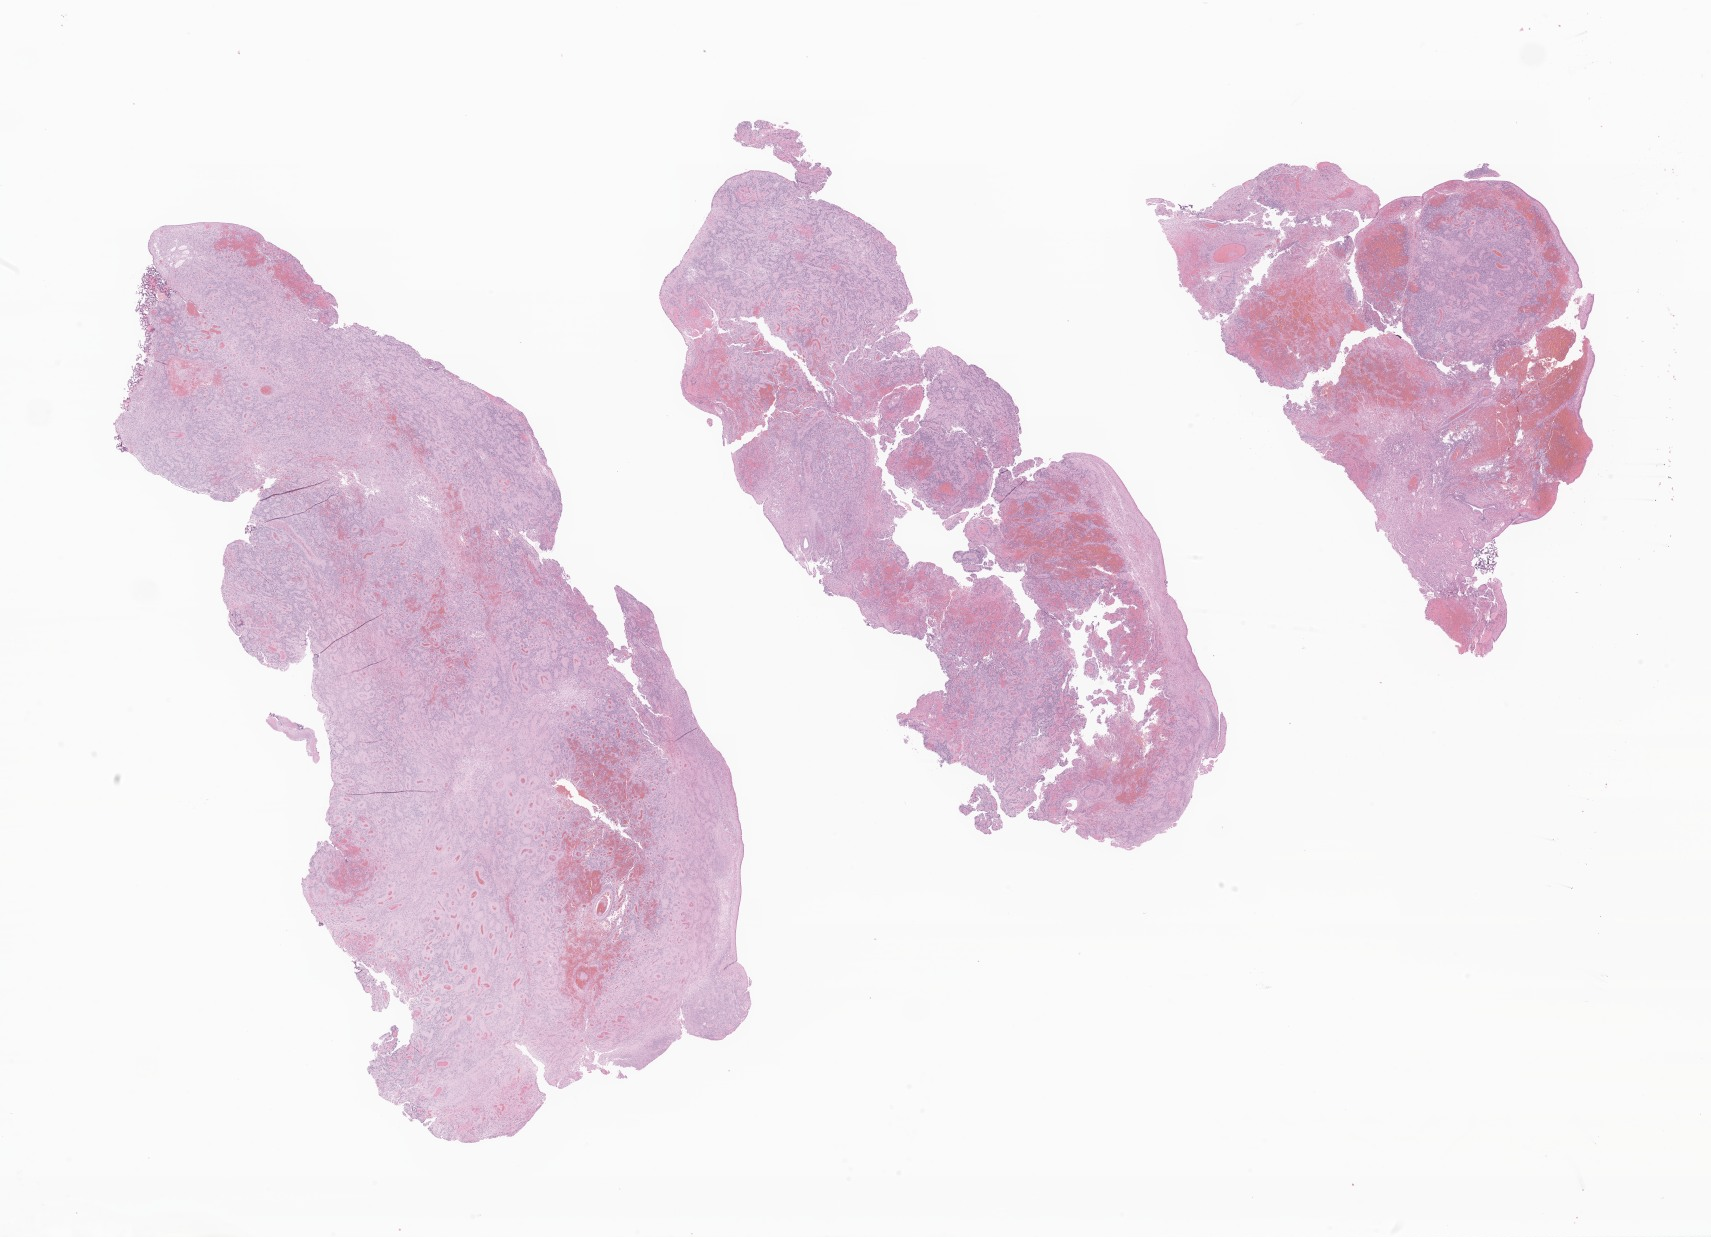
Hematoxylin and eosin (H&E) whole-slide image of tumor tissue from the brain, whole scanned area (about 28.9 x 20.9 mm) shown as a low-resolution overview. Formalin-fixed paraffin-embedded section. Patient male; age 433 days (about 1.2 years).
* diagnosis: Ependymoma, NOS